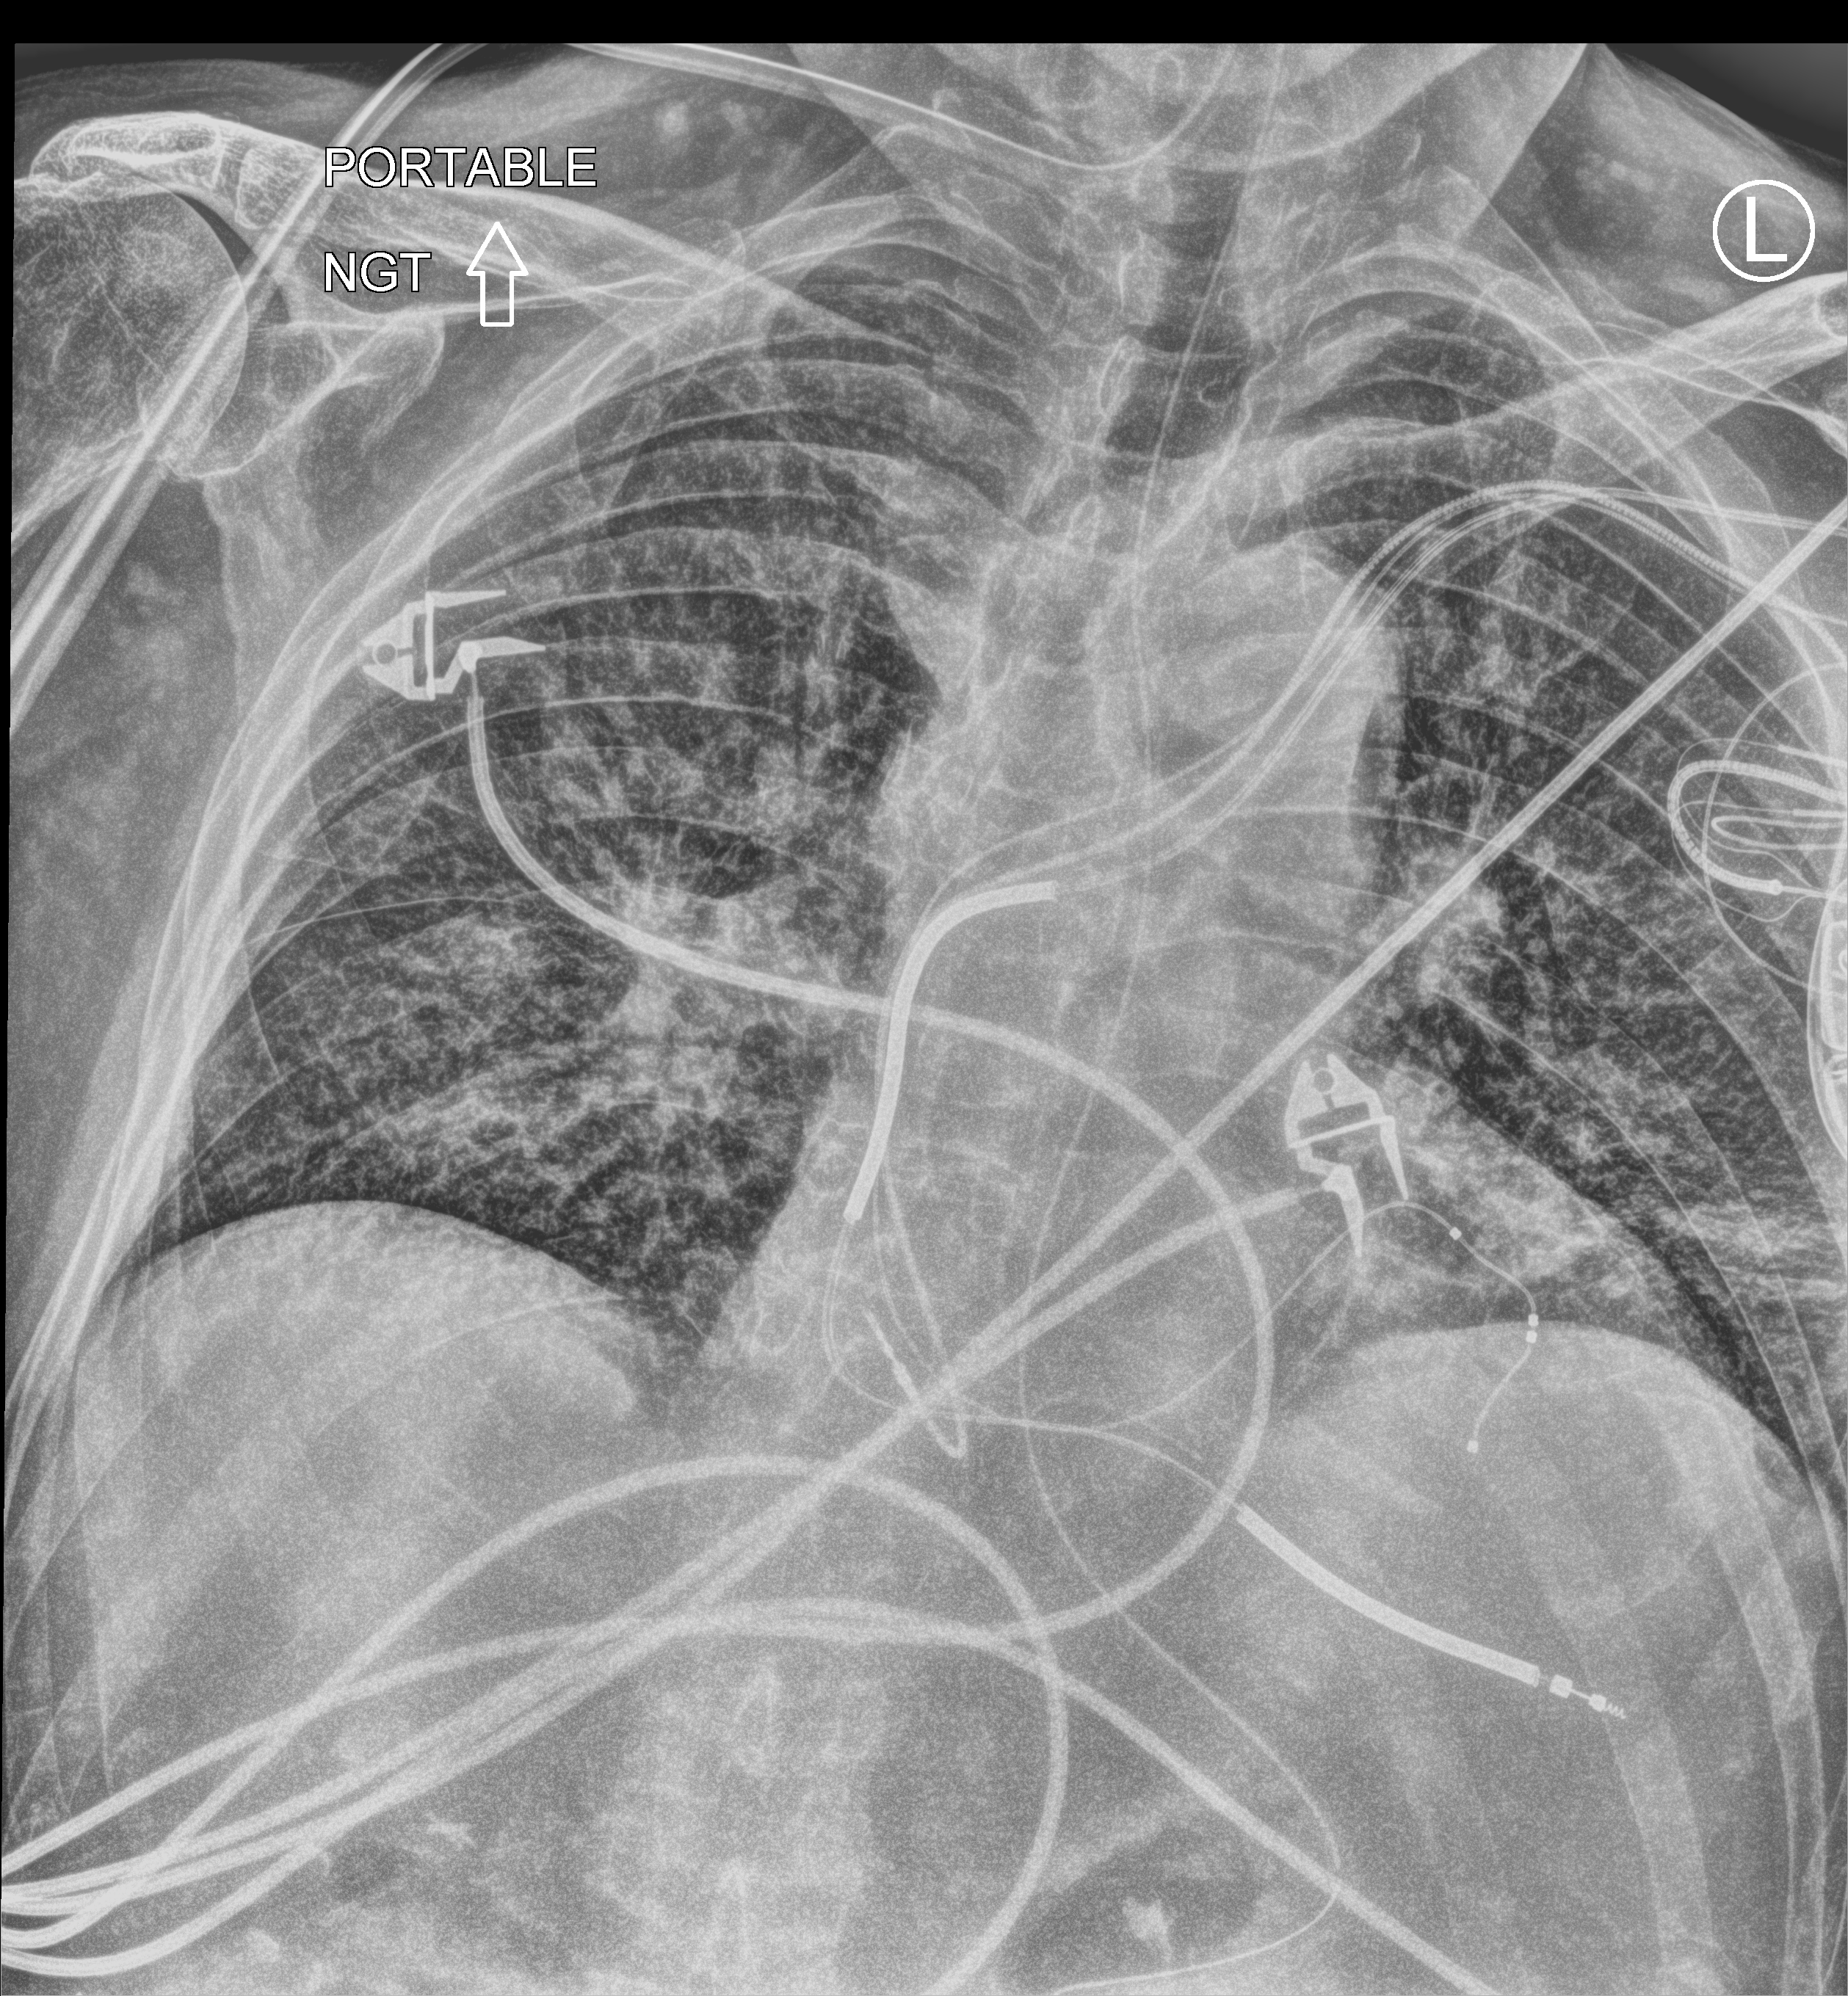
Chest X-ray (portable); anteroposterior (AP) projection. Patient hospitalised with COVID-19; male, aged 75–90 years.
Admission-level facts for this patient (not findings on this image; timing relative to this image not recorded):
- admitted to intensive care during this hospital stay: no